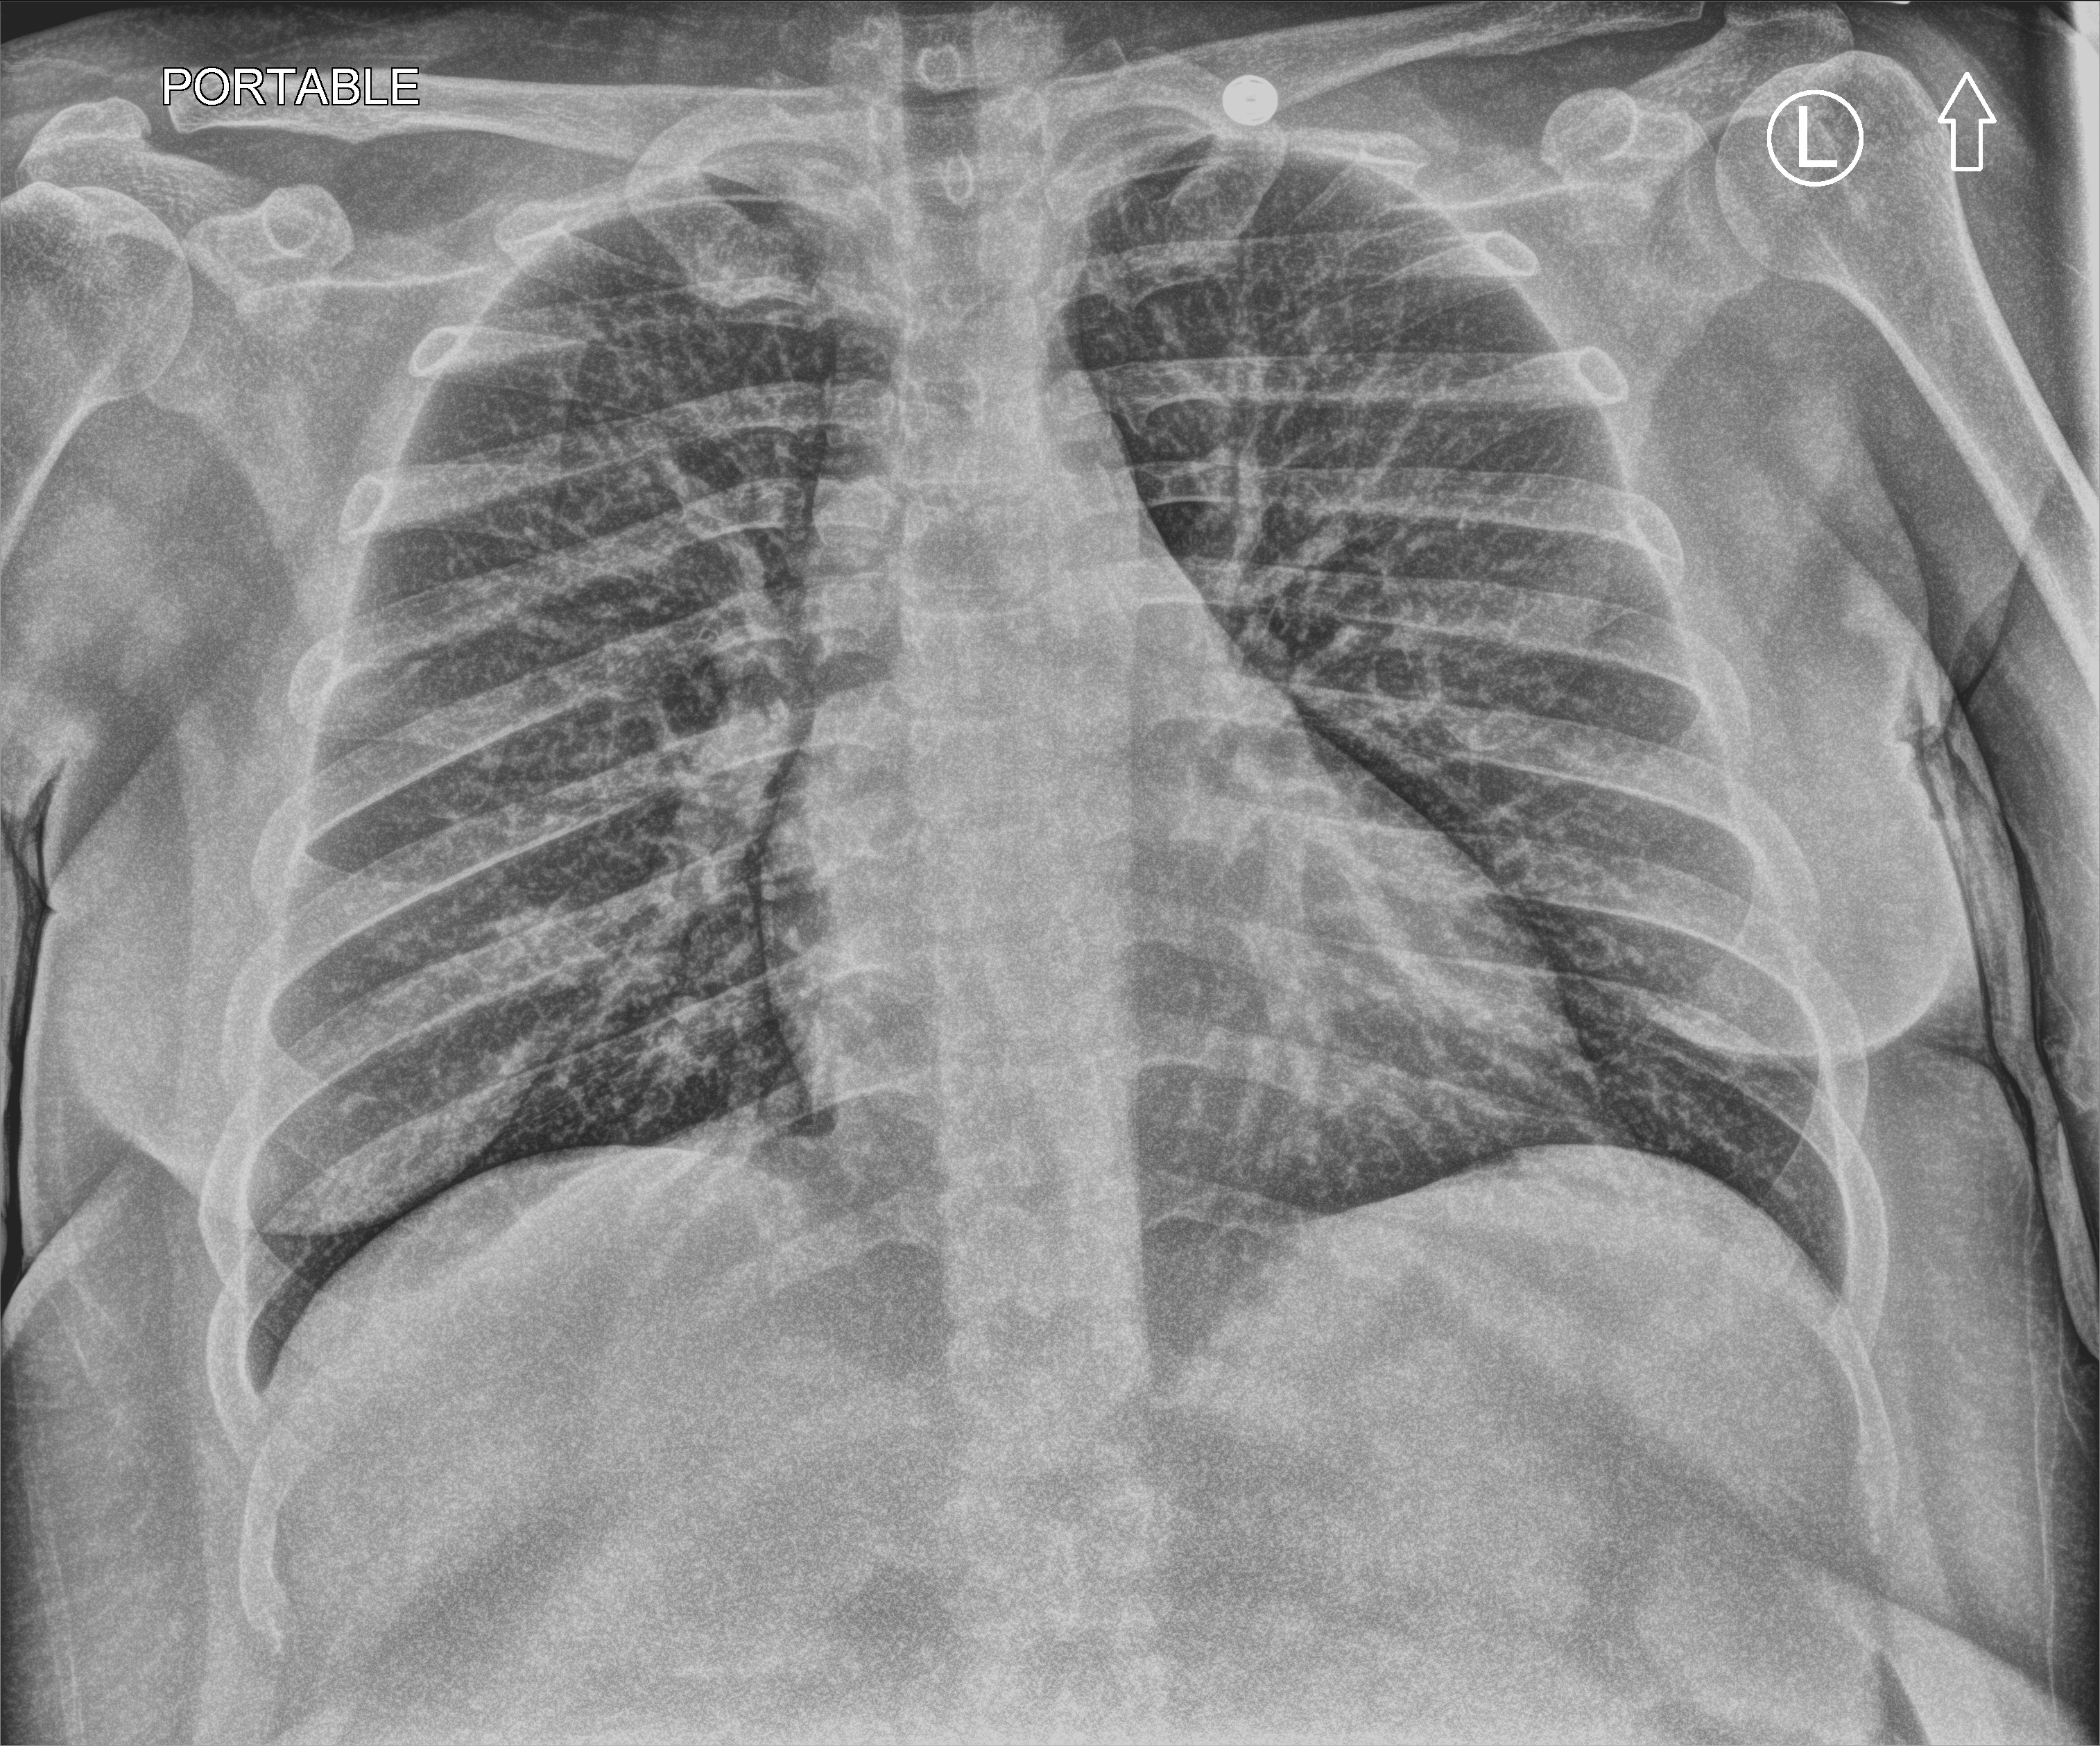
Chest X-ray (portable); anteroposterior (AP) projection. Female patient hospitalised with COVID-19, age 18–59 years.
Hospital-stay facts (about this admission, not read from this image; timing relative to this image not recorded):
- COPD (admission record): no
- diabetes (admission record): no
- length of hospital stay: 3 days